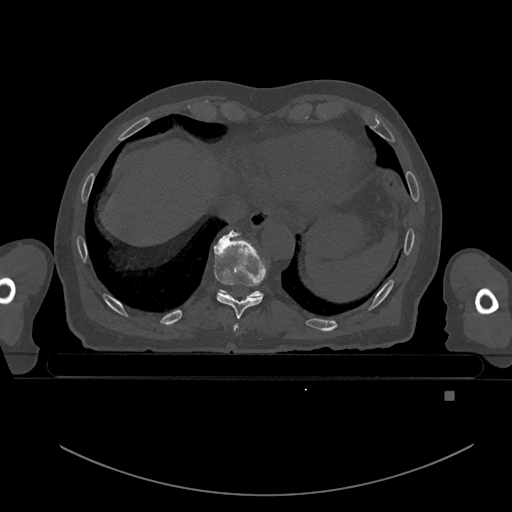
CT including the spine, one axial slice. Position 133 of 969 along the scan axis. Bone window (W 1800 / L 400 HU). 0.5 mm slice thickness. 512 × 512 image matrix, field of view 456 × 456 mm. Patient: male, 82 years. Case-level facts recorded for this patient, not image findings: primary cancer: prostate; vertebrae with lytic lesions (as recorded): T11, T9, T8, T2.
Structures marked on this image (semi-automatic segmentation, software-assisted and operator-edited):
- T10 vertebra: bounding box (x1, y1, x2, y2) in pixels: (253, 291, 261, 296)
- T8 vertebra: (233, 324, 239, 332)
- T9 vertebra: (214, 230, 268, 319)